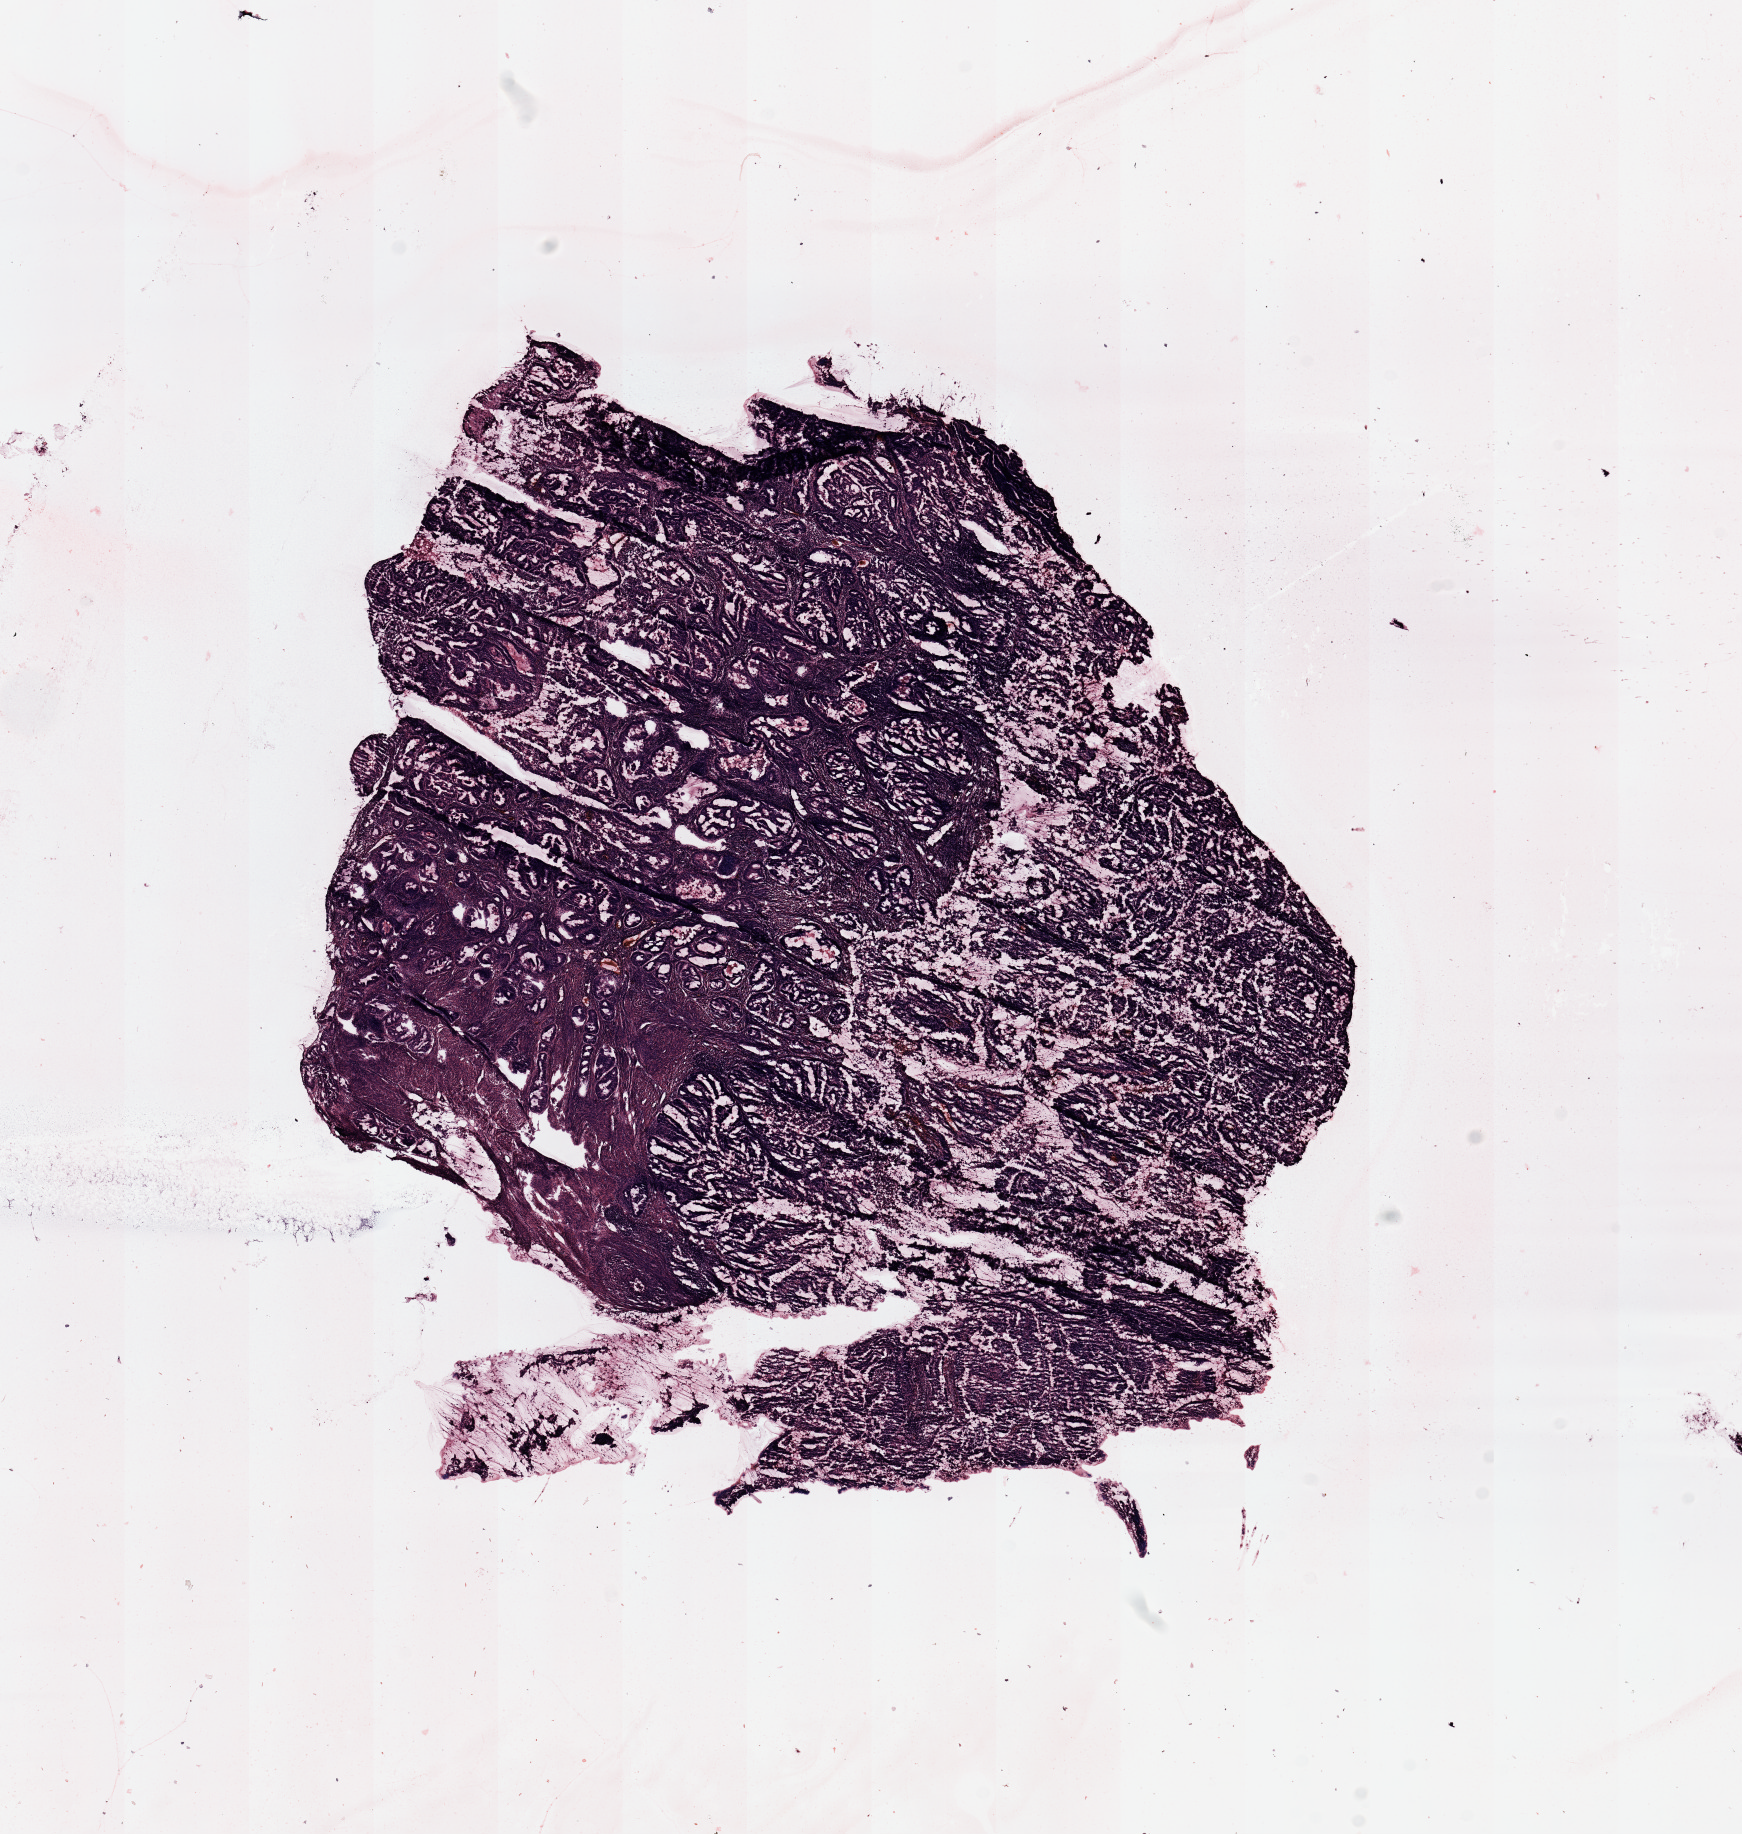
H&E whole-slide image, whole scanned area (about 13.8 x 14.5 mm) shown as a low-resolution overview, uterus, tumour tissue. 66-year-old female patient.
Histologic diagnosis: Endometrioid adenocarcinoma, NOS.